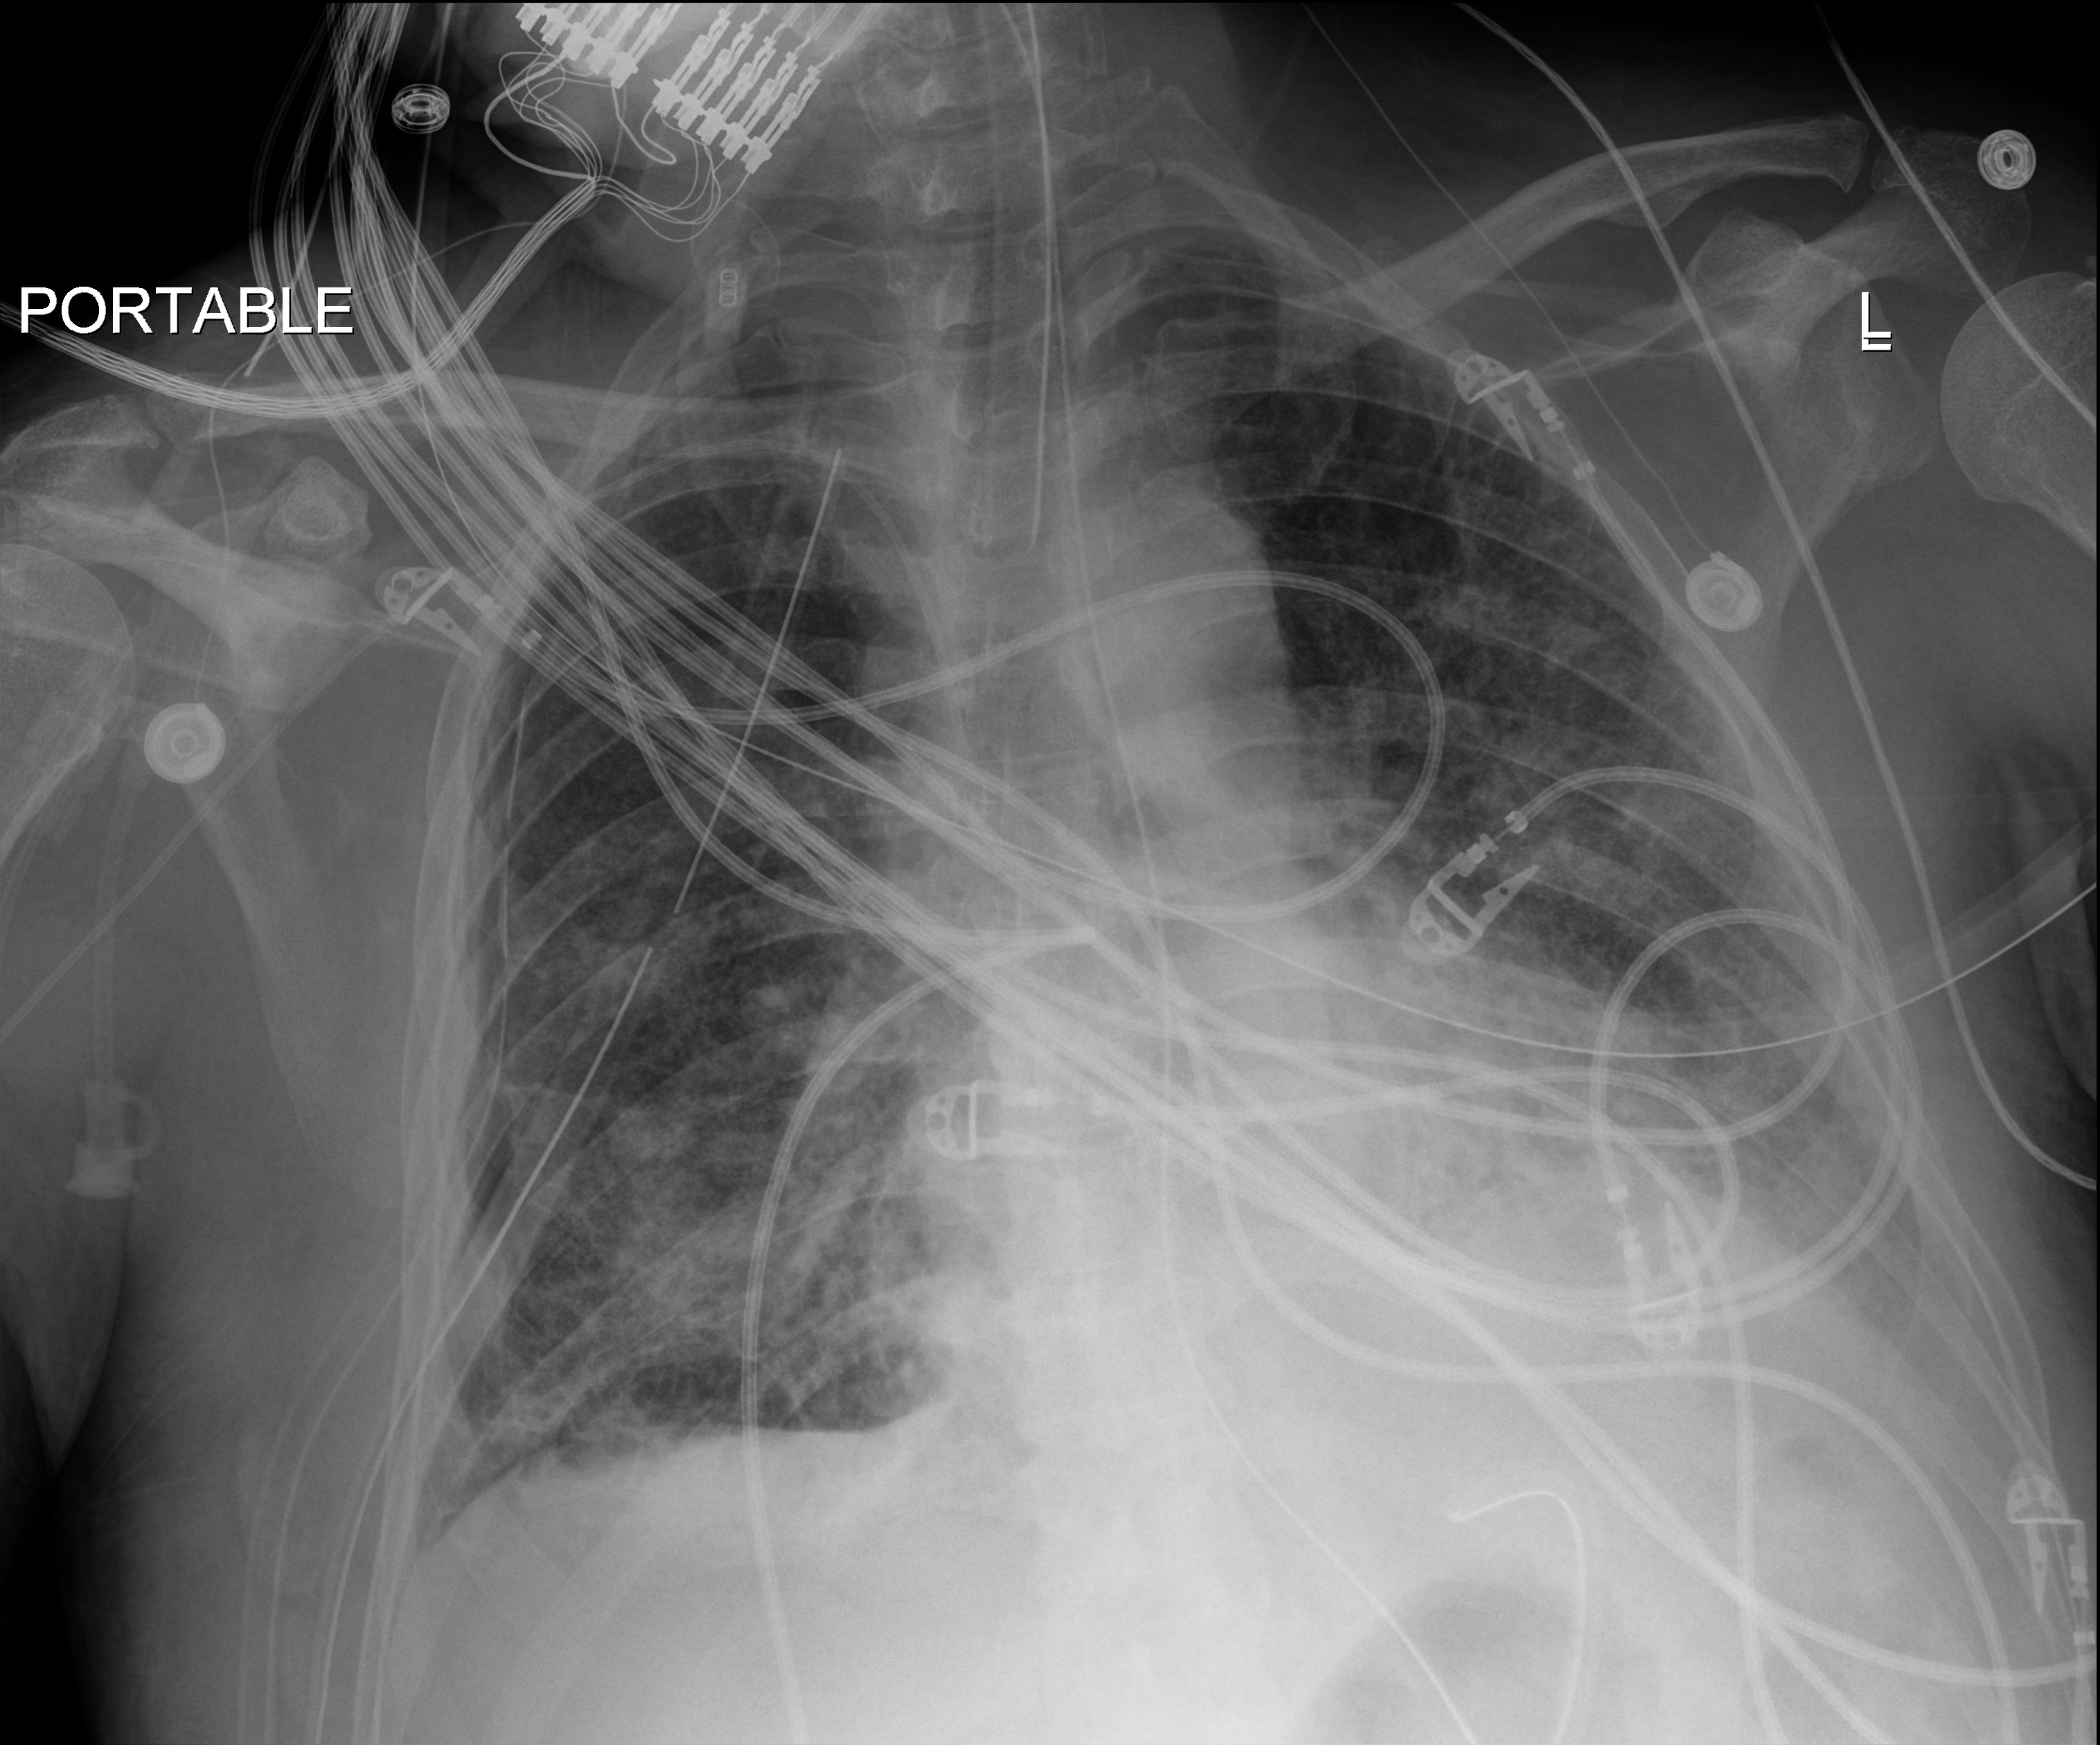
Bedside chest radiograph (digital radiography), anteroposterior (AP) projection. Male patient hospitalised with COVID-19, age 60–74 years.
Hospital-stay facts (about this admission, not read from this image; timing relative to this image not recorded):
- mechanically ventilated during this hospital stay: yes